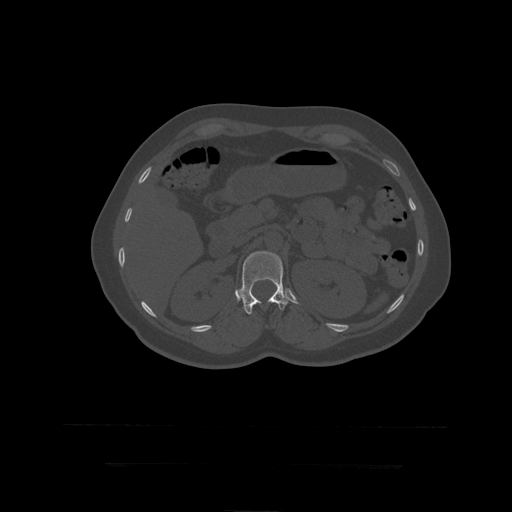
CT including the spine, one axial slice. Slice 176 of 399 in the series (ordered by position). 120 kVp. Bone window (W 1800 / L 400 HU). 1.25 mm slice thickness. 512 × 512 image matrix, field of view 450 × 450 mm. Patient age 41 years. From the clinical record (not read from this slice): primary cancer: breast.
Structures marked on this image (semi-automatically segmented with operator editing):
- L1 vertebra: box from (x=240, y=251) to (x=290, y=315) px